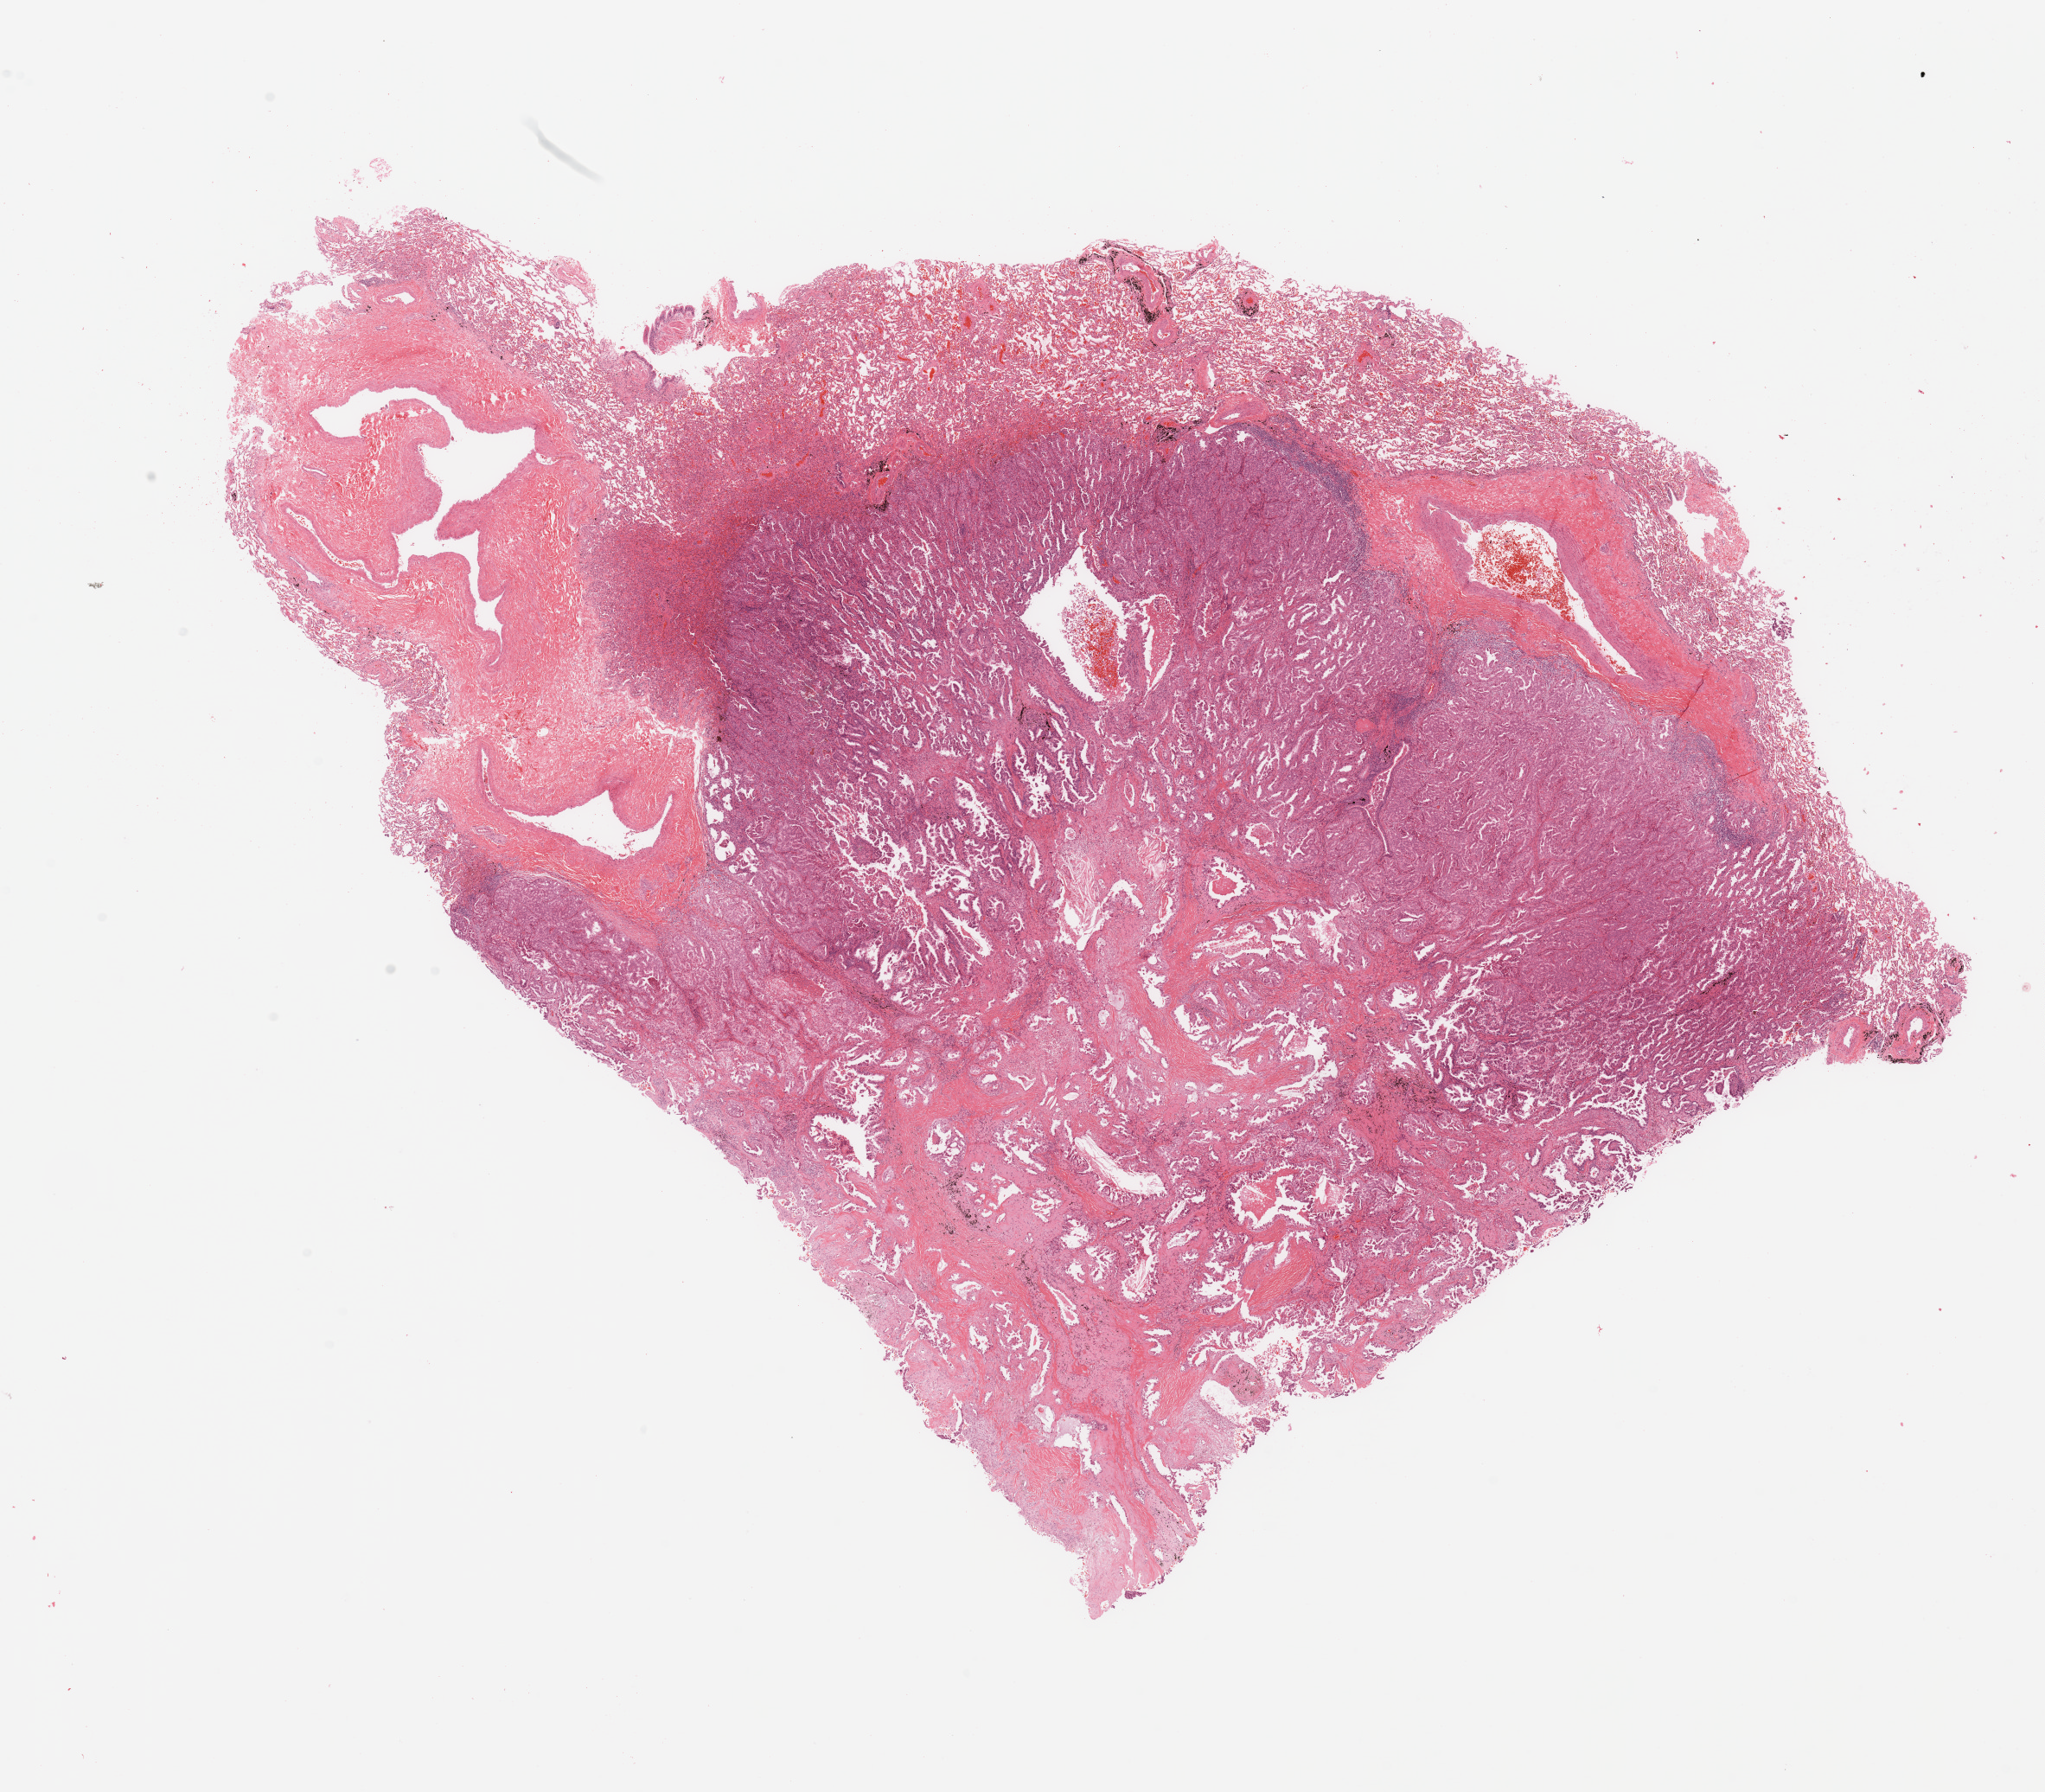
Whole-slide histology image, H&E, shown as a low-resolution overview of the whole scanned area (about 18.7 x 16.4 mm, slide scanned at 20x); tumour tissue sample, lung. Female, 44 y/o. Histologic grade: G2 (moderately differentiated).
AJCC pathologic stage: IIIA. Histologic diagnosis: Adenocarcinoma, NOS.